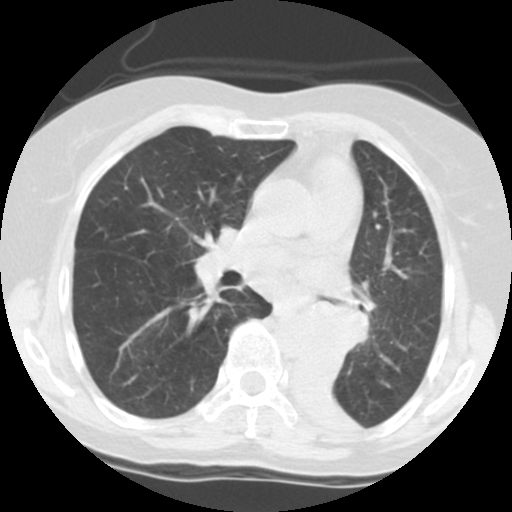
Chest CT (low-dose screening protocol), one axial image. Third screening round (two years after baseline). Lung window (W 1500 / L -600 HU). 140 kVp. 512 × 512 image matrix, field of view 280 × 280 mm. Female participant, aged 56 years at enrolment. Former smoker at enrolment.
- Expert reader's lesion annotation, bounding box [x1, y1, x2, y2] px = [311, 298, 370, 351].
- No non-calcified nodule or mass ≥4 mm was recorded by the screening reader at this exam.